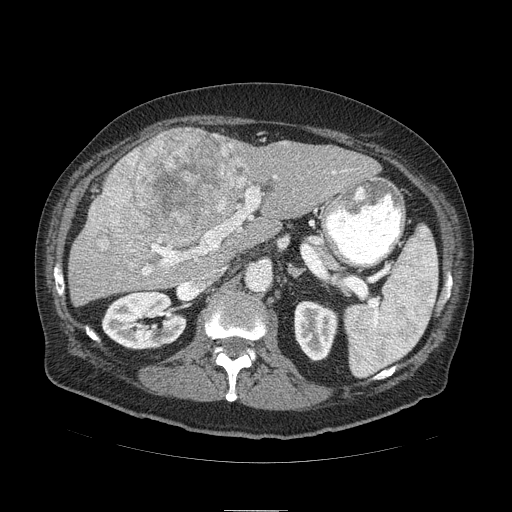
Contrast-enhanced abdominal CT (liver protocol), one axial slice. Position 49 of 103 along the scan axis. Soft-tissue window (W 400 / L 40 HU). 2.5 mm slice thickness. 512 × 512 image matrix. From the clinical record (not read from this slice): diagnosis: hepatocellular carcinoma (patient treated with transarterial chemoembolisation; whether this scan precedes or follows treatment is not stated here); TNM stage (as recorded): Stage-IIIA; Child-Pugh class: B; tumour differentiation: well differentiated; tumour nodularity: multinodular.
Outlined on this slice (semi-automatically segmented with operator editing):
- liver parenchyma outside the tumour (the mass and vessels are separate outlines, so this box may not span the whole liver): bounding box (x1, y1, x2, y2) in pixels: (68, 128, 379, 306)
- mass: (85, 128, 255, 272)
- liver vessels: (127, 154, 345, 275)